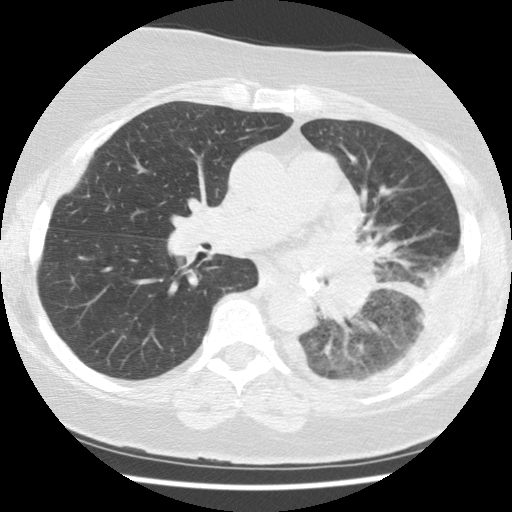
Chest CT (low-dose screening protocol), one axial image; baseline screening round; lung window (W 1500 / L -600 HU); 2.5 mm slice thickness; slice 54 of 114 in the series. Female participant, aged 65 years at enrolment. Current smoker at enrolment.
Expert reader's lesion annotation, bounding box [x1, y1, x2, y2] px = [297, 283, 394, 358]. The exam's reader record, not a measurement of the box and not confirmed to be the same lesion: non-calcified nodule or mass ≥4 mm, left lower lobe, 74 × 48 mm, spiculated (stellate) margins, soft tissue attenuation. Lung cancer was diagnosed 13 days after this screen: adenocarcinoma, NOS, left lower lobe, stage IV (AJCC 6th edition), 74 mm at pathology.